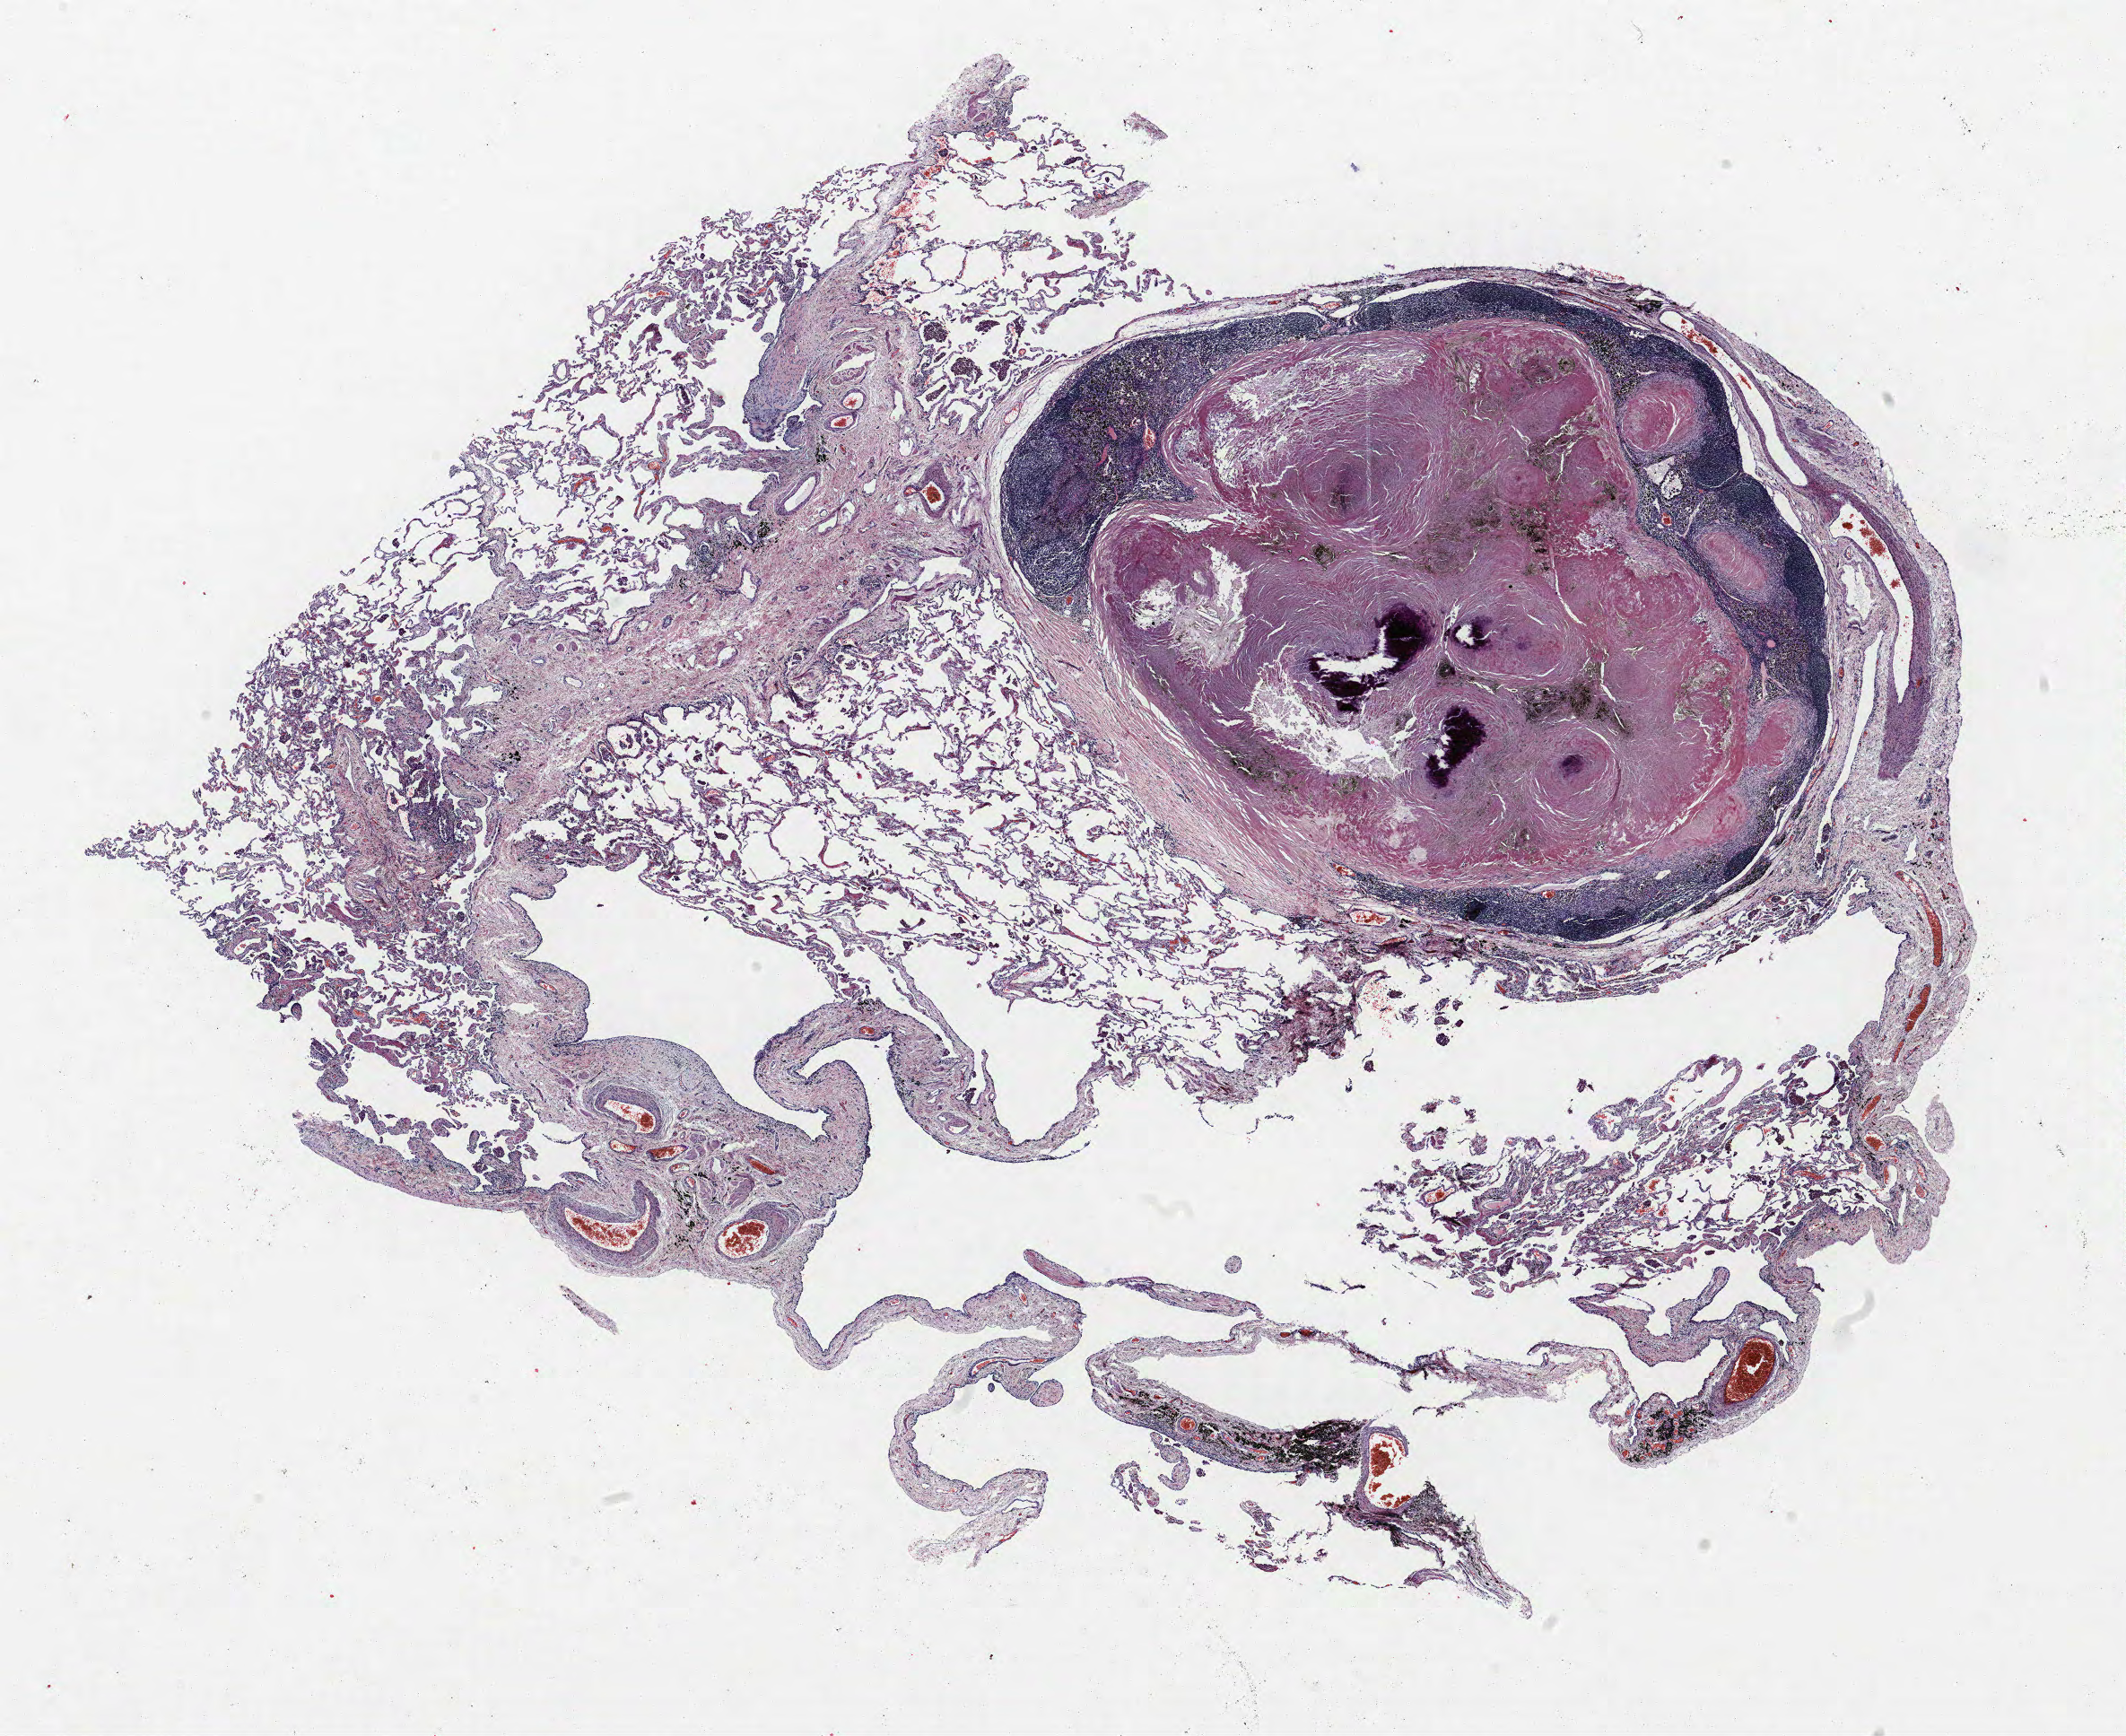
Whole-slide histology image, H&E, shown as a low-resolution overview of the whole scanned area (about 19.0 x 15.5 mm); formalin-fixed paraffin-embedded (FFPE) section; lung. Male patient, aged 58 at enrolment. Current smoker at enrolment.
Participant's lung-cancer diagnosis: Adenocarcinoma, NOS (ICD-O-3 8140/3).